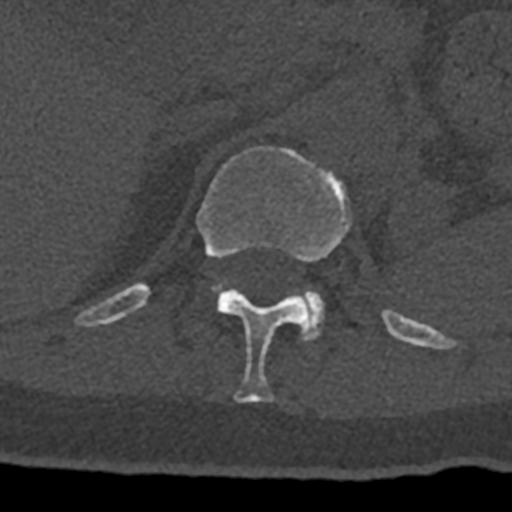
CT including the spine, one axial slice; slice 481 of 797 in the series (ordered by position); 120 kVp; bone window (W 1800 / L 400 HU); 512 × 512 image matrix, field of view 160 × 160 mm. Patient: male, 74 years. From the clinical record (not read from this slice): primary cancer: renal.
Structures marked on this image (semi-automatically segmented with operator editing):
- L1 vertebra: bounding box <214,285,324,340> (left, top, right, bottom; pixels)
- T12 vertebra: <75,146,432,403>